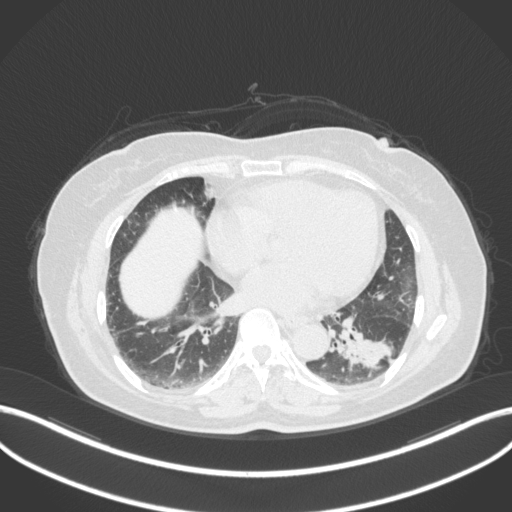
Chest CT, one axial slice; slice 148 of 307 in the series (ordered by position); 120 kVp; lung window (W 1500 / L -600 HU); 1 mm slice thickness; 512 × 512 image matrix. Female patient, age 59 years. From the clinical record (not read from this slice): clinical TNM (as recorded): T2a N0 M0; histopathological grade: G2-3.
Outlined on this slice (bounding box drawn by a radiologist):
- lung tumour (recorded histology: adenocarcinoma): bounding box [x1, y1, x2, y2] px = [329, 314, 398, 373]